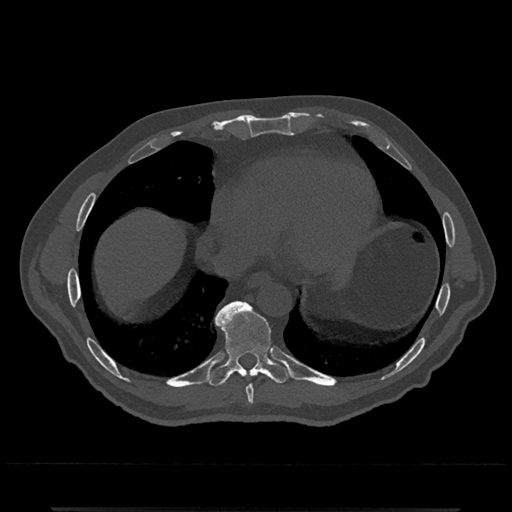
CT including the spine, one axial slice; position 627 of 797 along the scan axis; reconstruction kernel Br40s/3; bone window (W 1800 / L 400 HU); 512 × 512 image matrix, field of view 393 × 393 mm. Male patient, age 67 years. Case-level facts recorded for this patient, not image findings: primary cancer: prostate.
Annotated regions visible in this slice (semi-automatically segmented with operator editing):
- T8 vertebra: bounding box [x1, y1, x2, y2] px = [246, 385, 254, 404]
- T9 vertebra: [206, 301, 292, 387]